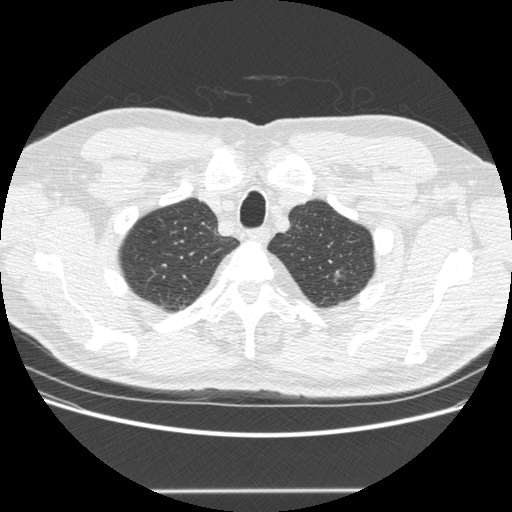
Axial slice from a low-dose chest CT screening exam, second annual screen, lung window (W 1500 / L -600 HU), standard (soft-tissue) reconstruction kernel (STANDARD), 120 kVp, slice 48 of 223 in the series. Male, age 69 years at enrolment.
Expert reader's lesion annotation, bounding box (x1, y1, x2, y2) in pixels: (312, 262, 347, 294). Screening reader's record for this exam: no non-calcified nodule ≥4 mm recorded. Official screen result: negative screen, significant abnormalities not suspicious for lung cancer.